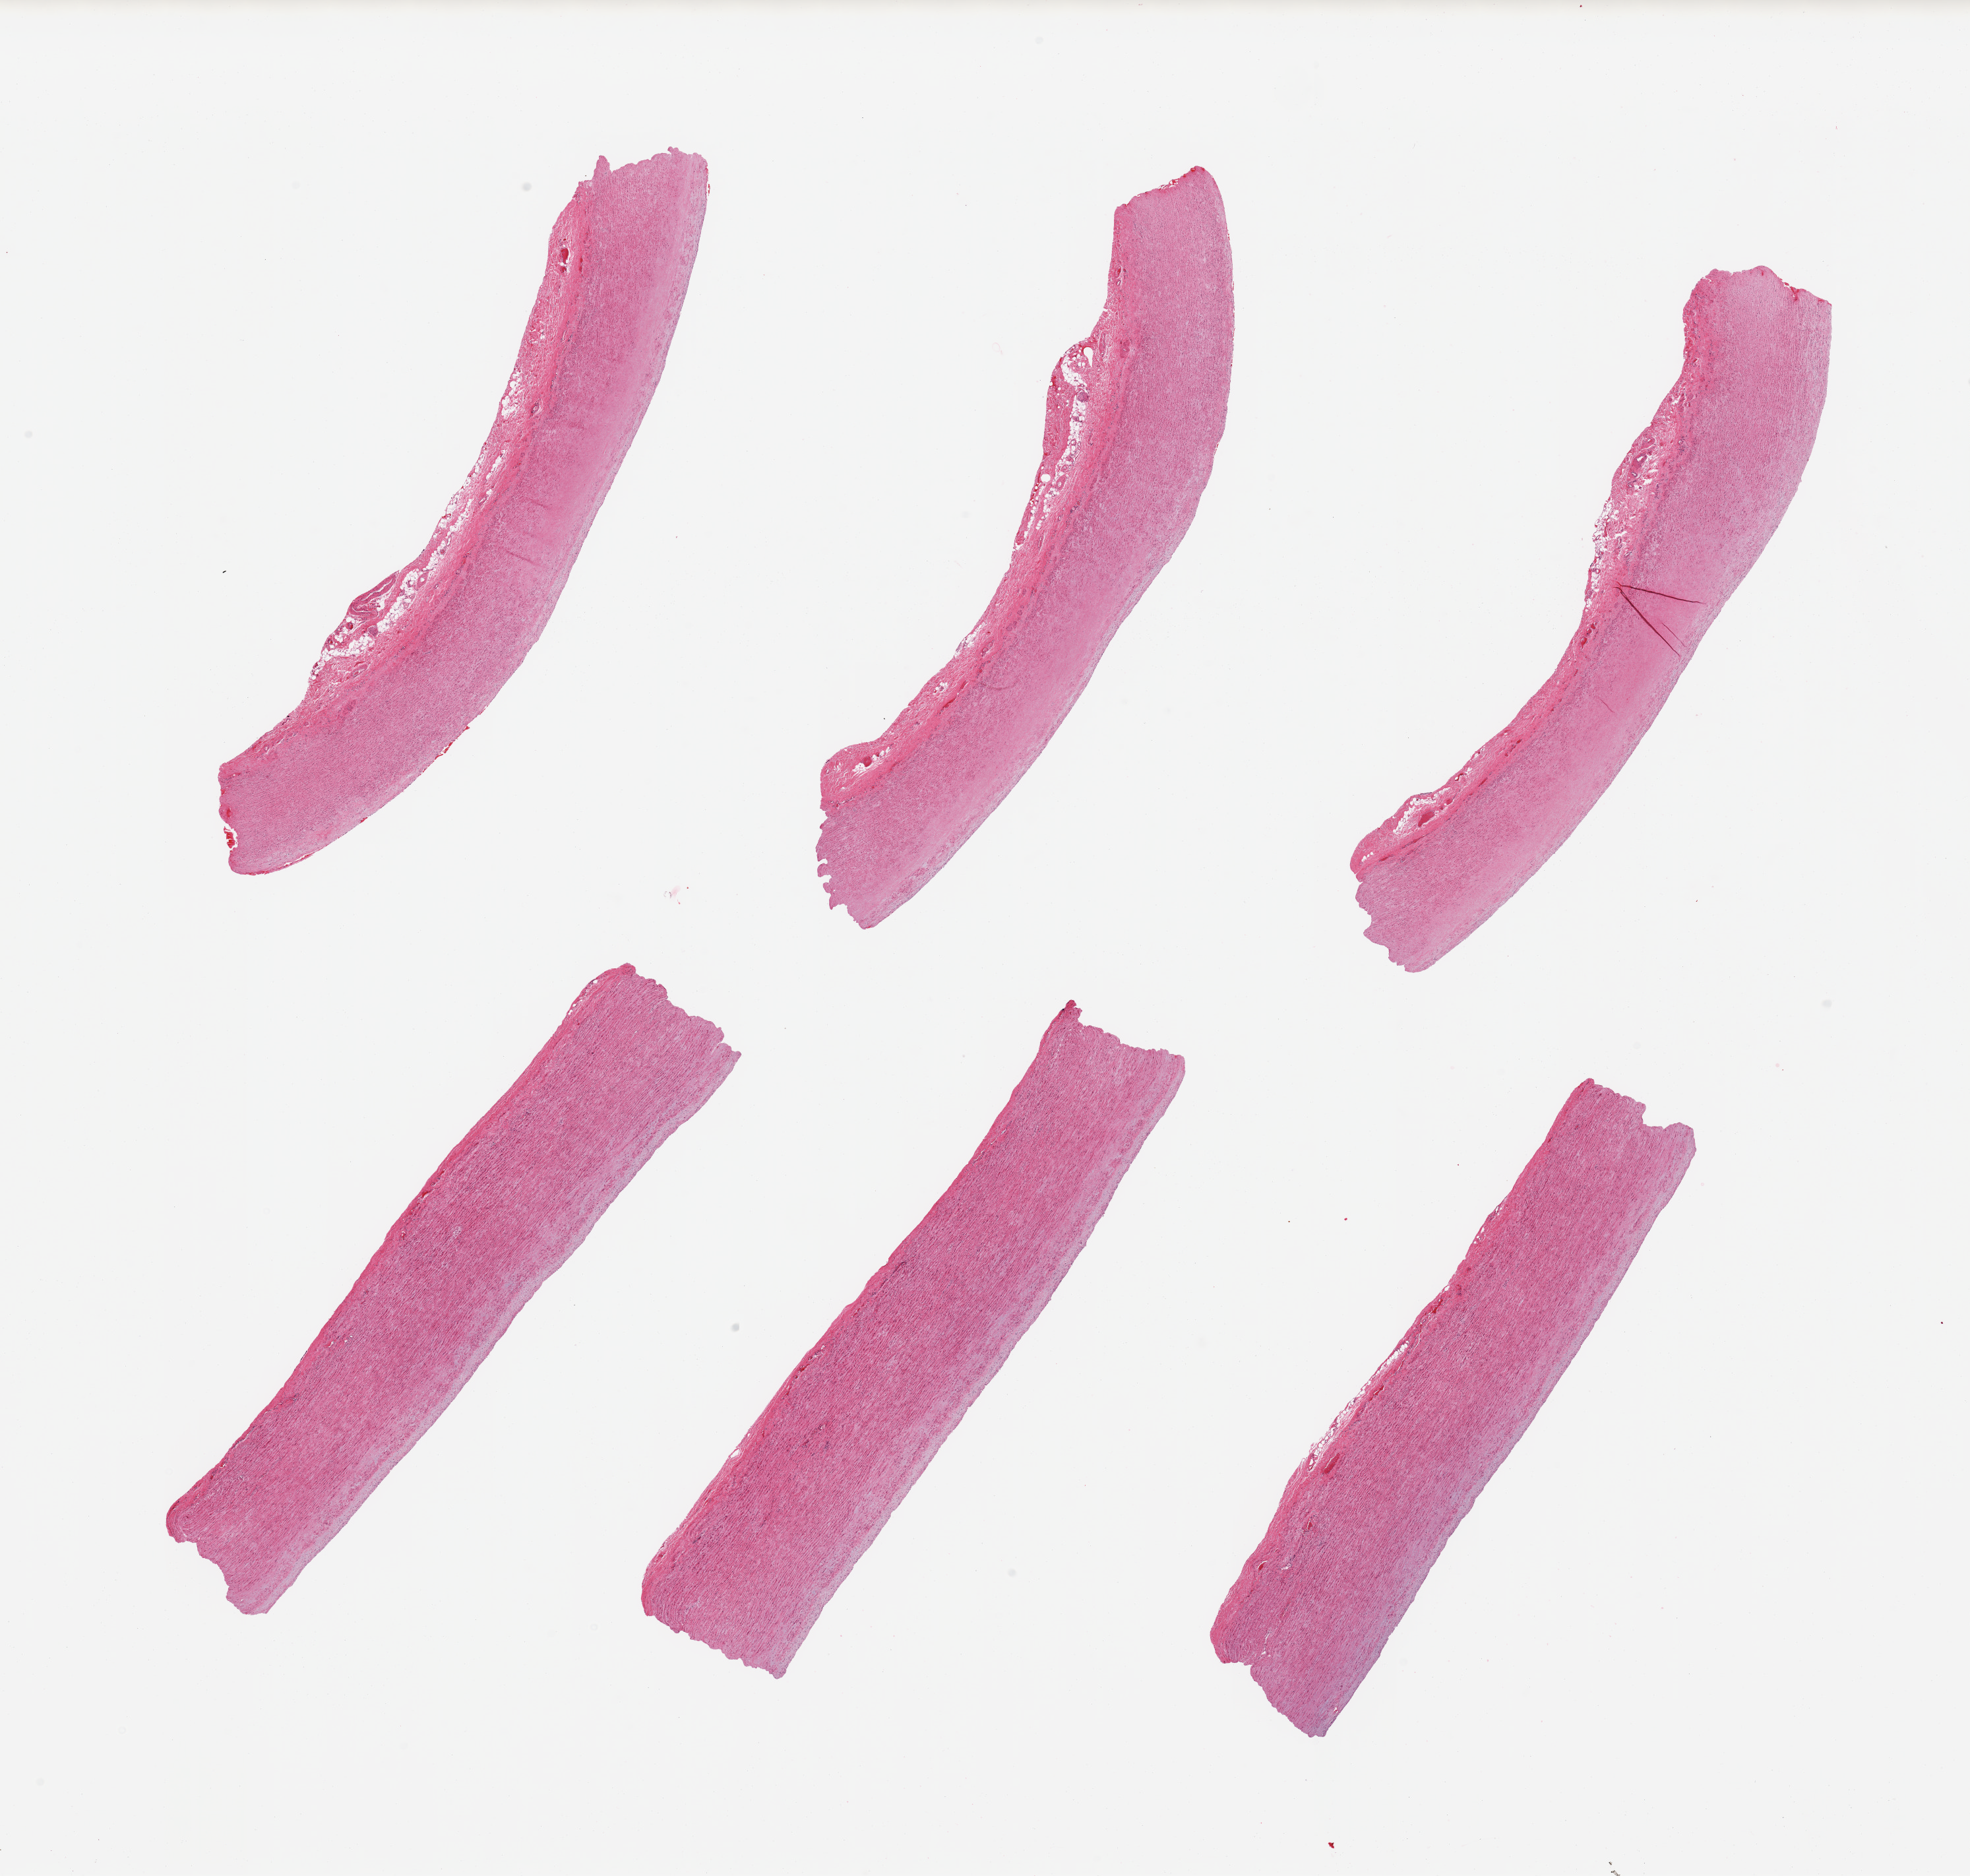
Digitized H&E-stained section — whole scanned area (about 23.6 x 22.5 mm, from a 20x scan) shown as a low-resolution overview. PAXgene-fixed paraffin-embedded (PFPE) section. Sampled site (target tissue): aorta. Donor tissue sample. Female donor.
• review note (as recorded): 6 pieces, trace atherosis